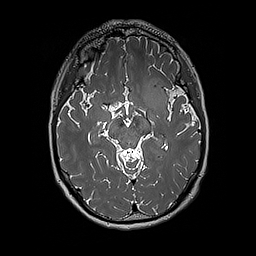
Brain MRI from a brain-tumour surgery series, one axial slice. Slice 111 of 192 in the series (ordered by position). 256 × 256 image matrix, field of view 250 × 250 mm. From the clinical record (not read from this slice): histopathology: Glioblastoma; WHO grade: 4; IDH mutation: no; tumour location: Left Insular.
Structures marked on this image (manually delineated by an expert):
- tumour: bounding box (x1, y1, x2, y2) in pixels: (142, 78, 170, 112)